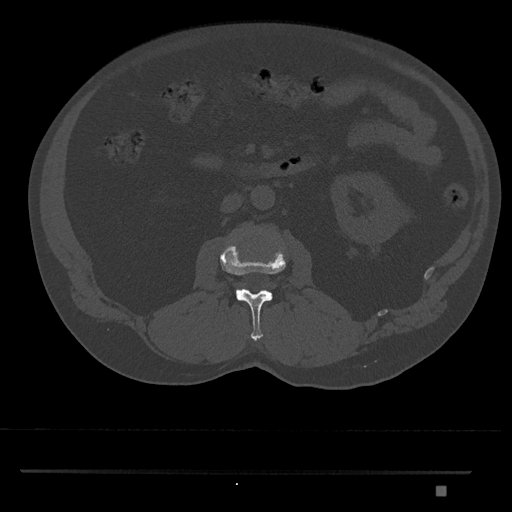
CT including the spine, one axial slice. Slice 735 of 1134 in the series (ordered by position). 120 kVp. Bone window (W 1800 / L 400 HU). 0.5 mm slice thickness. 512 × 512 image matrix. Patient: male, 65 years. From the clinical record (not read from this slice): primary cancer: prostate.
Outlined on this slice (semi-automatic segmentation, software-assisted and operator-edited):
- L2 vertebra: bounding box (x1, y1, x2, y2) in pixels: (220, 243, 286, 341)